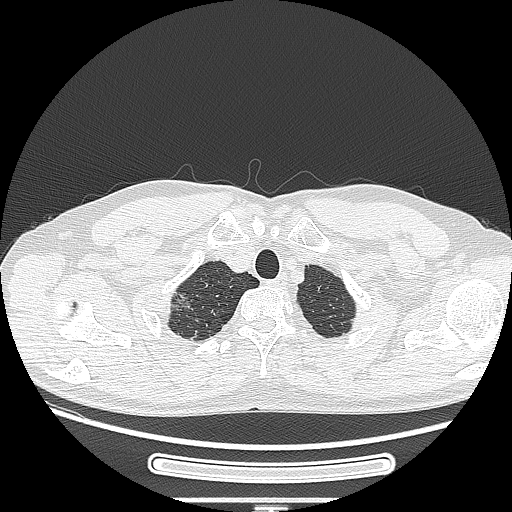
Chest CT, one axial slice; reconstruction kernel LUNG; 120 kVp; lung window (W 1500 / L -600 HU); 1.25 mm slice thickness; 512 × 512 image matrix. Male patient, age 53 years. From the clinical record (not read from this slice): clinical TNM (as recorded): T1c N0 M0; histopathological grade: G2.
Outlined on this slice (bounding box drawn by a radiologist):
- lung tumour (recorded histology: adenocarcinoma): box from (x=160, y=282) to (x=196, y=319) px